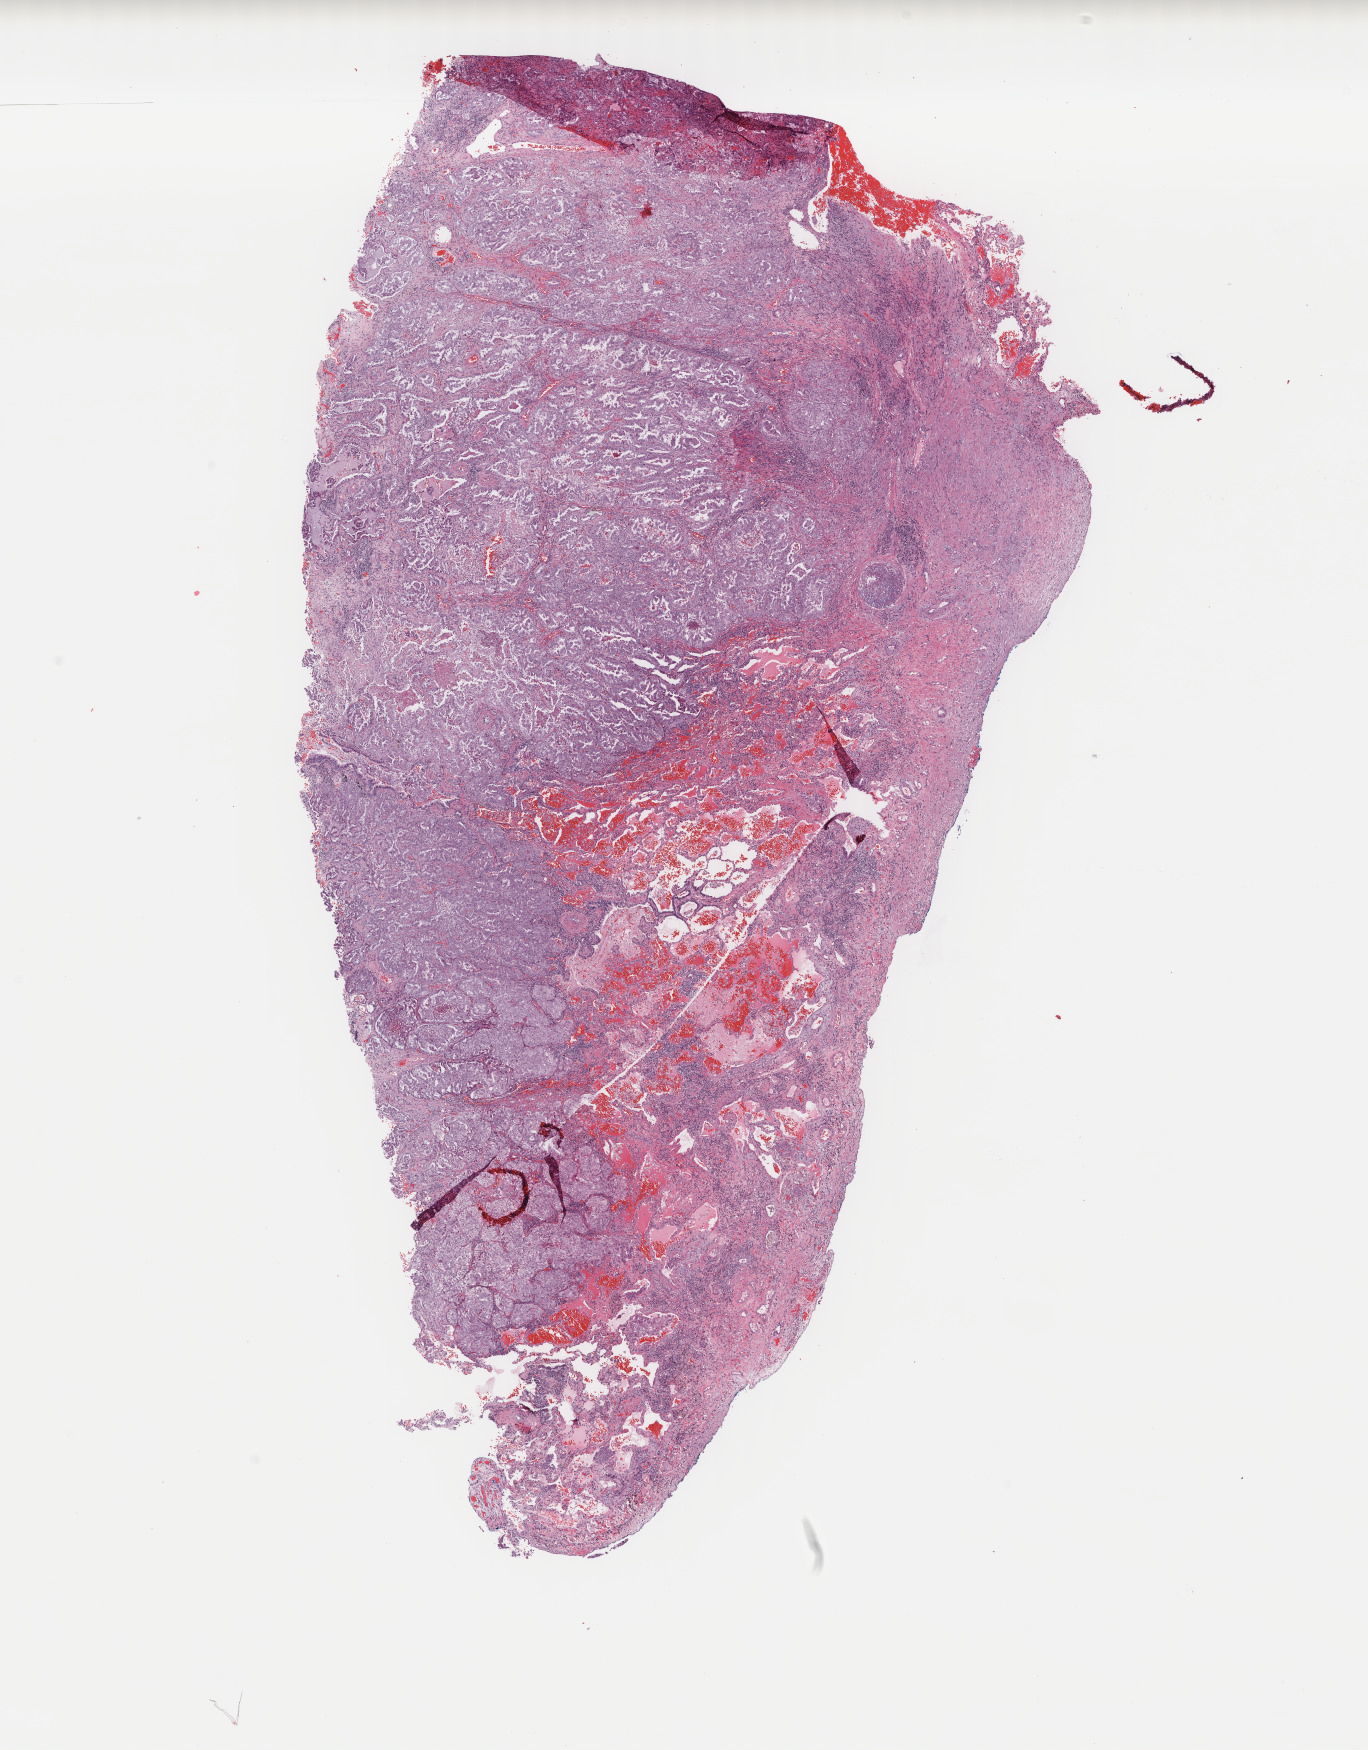
Whole-slide histology image, H&E-stained, shown as a low-resolution overview of the whole scanned area (about 10.9 x 13.9 mm); frozen section; primary tumour sample from the lung. Female, age 60 years at initial diagnosis. Slide review estimates, as recorded: tumour cells 70%, tumour nuclei 70%, normal cells 1%, stromal cells 27%, necrosis 2%. Inflammatory infiltration, as recorded: lymphocyte infiltration 4%, monocyte infiltration 1%, neutrophil infiltration 3%.
- laterality: right
- TNM: T2a N0 M0
- diagnosis: Adenocarcinoma, NOS
- AJCC pathologic stage: IB (6th edition)